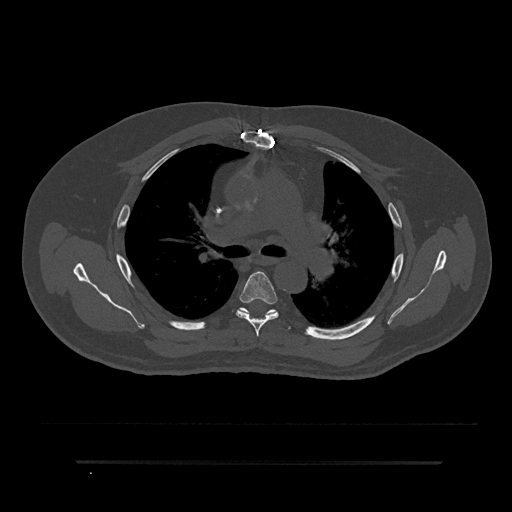
CT including the spine, one axial slice; position 564 of 797 along the scan axis; reconstruction kernel Br40s/3; 120 kVp; bone window (W 1800 / L 400 HU); 512 × 512 image matrix, field of view 464 × 464 mm. Patient: male, 59 years. Case-level facts recorded for this patient, not image findings: primary cancer: bile ducts.
Annotated regions visible in this slice (semi-automatic segmentation, software-assisted and operator-edited):
- T5 vertebra: bounding box [x1, y1, x2, y2] px = [236, 271, 279, 337]
- T6 vertebra: [239, 308, 291, 329]